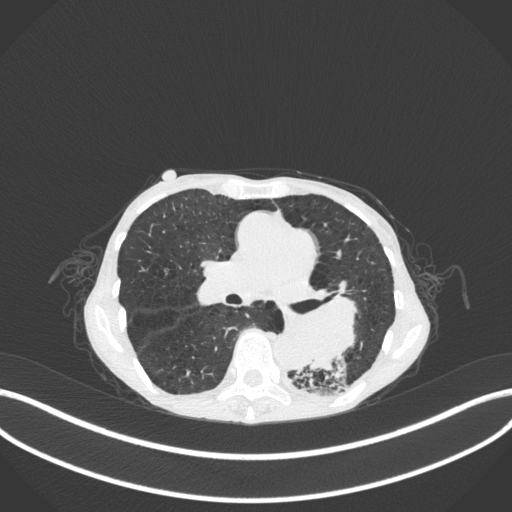
Chest CT, one axial slice; slice 151 of 347 in the series (ordered by position); reconstruction kernel B31f; 120 kVp; lung window (W 1500 / L -600 HU); 1 mm slice thickness; 512 × 512 image matrix. Patient: female, 70 years. From the clinical record (not read from this slice): clinical TNM (as recorded): T3 N0 M0.
Structures marked on this image (bounding box drawn by a radiologist):
- lung tumour (recorded histology: small cell carcinoma): bounding box (x1, y1, x2, y2) in pixels: (273, 293, 363, 373)